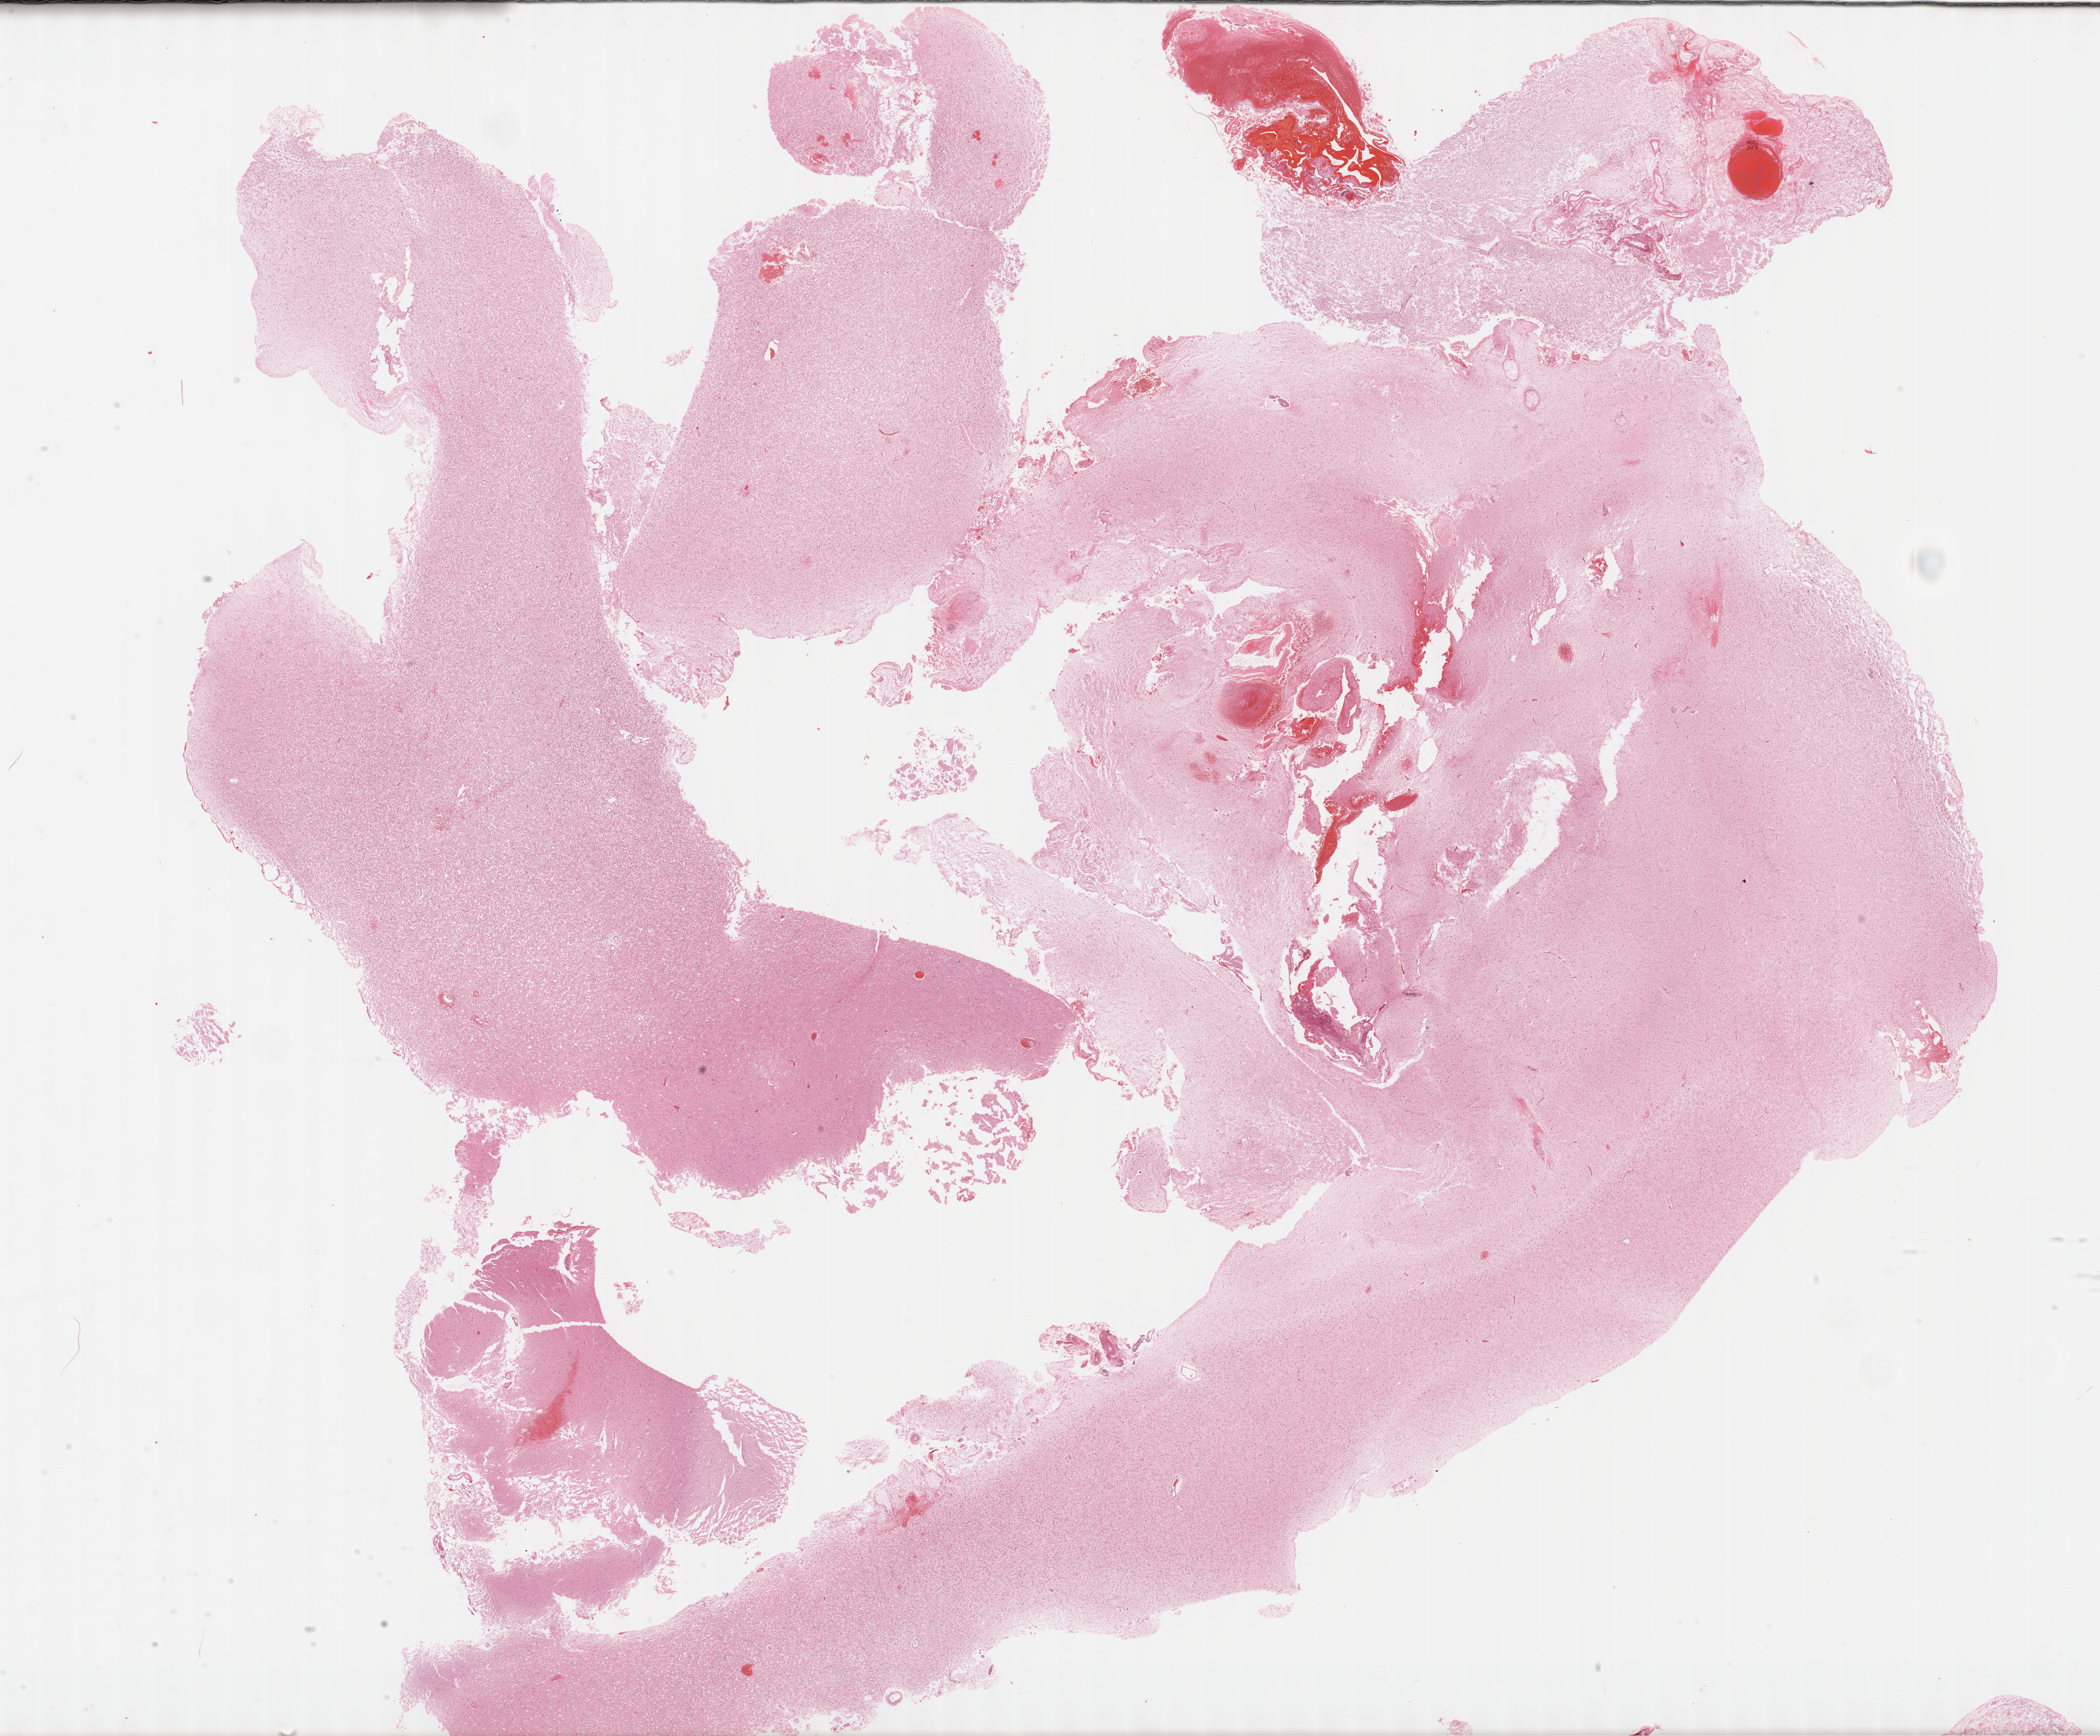
H&E whole-slide image, low-resolution overview of the scanned area, about 28.2 x 23.3 mm. FFPE section. Brain, primary tumour sample. Male patient; age at initial diagnosis 31 years. Histologic grade: G2 (moderately differentiated).
Laterality: left. Diagnosis: Mixed glioma.